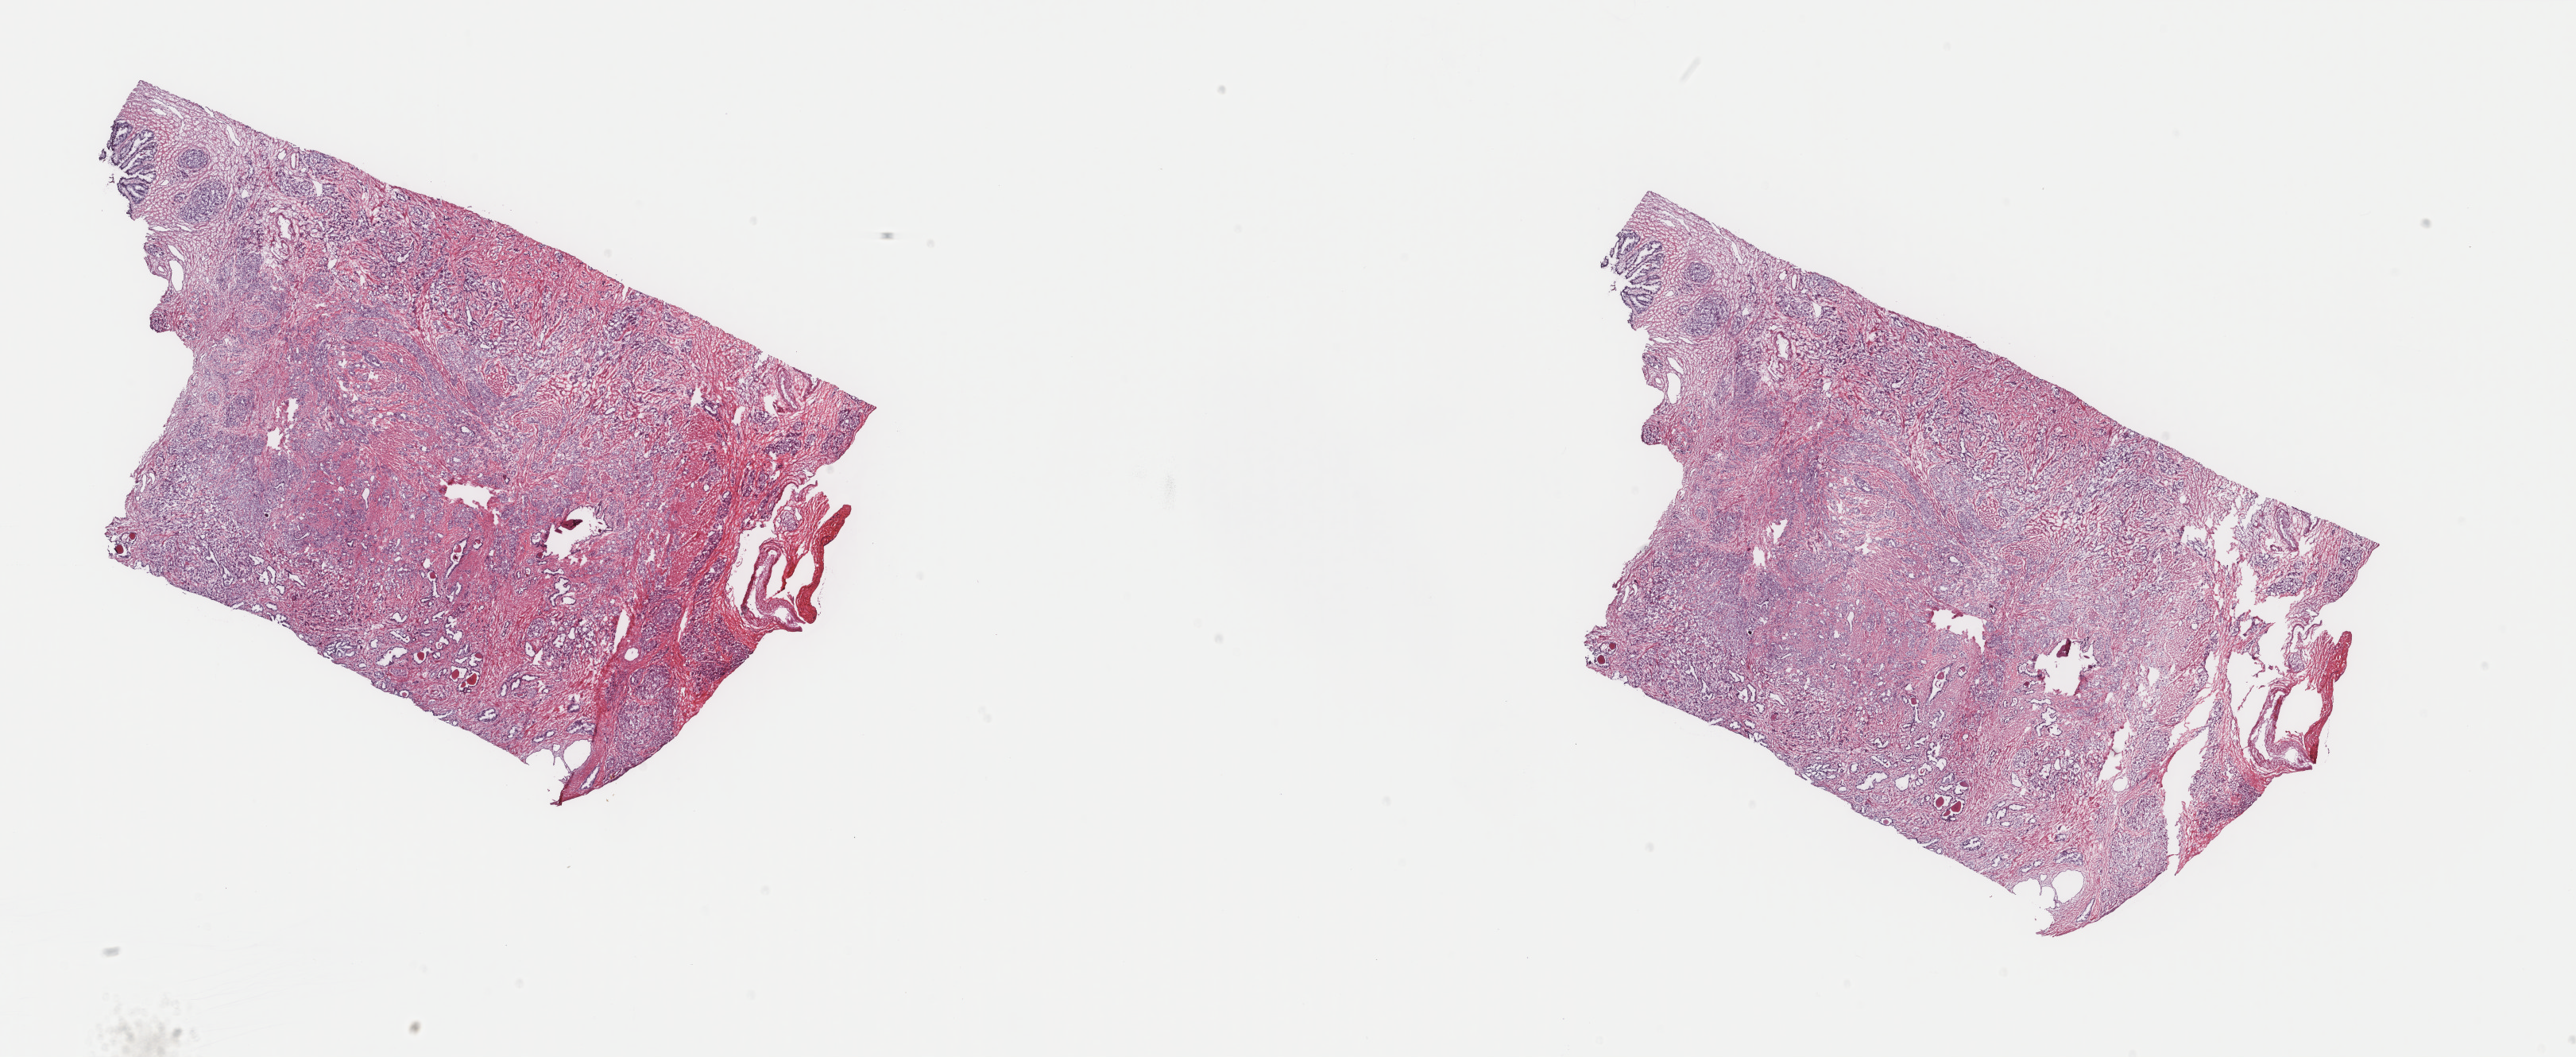
Whole-slide histology image, H&E, a low-resolution overview of the entire scanned area, about 25.7 x 10.6 mm; frozen section from the top of the tissue portion; primary tumour sample from the prostate. Male patient; age at initial diagnosis 55 years. Gleason score: 9 (4+5). Pathologist review of this section (percent, as recorded): tumour cells 45%, tumour nuclei 85%, normal cells 15%, stromal cells 40%, necrosis 0%. Infiltration values recorded for this section: lymphocyte infiltration 2%, monocyte infiltration 1%, neutrophil infiltration 0%.
Diagnosis: Adenocarcinoma with mixed subtypes (prostate gland).